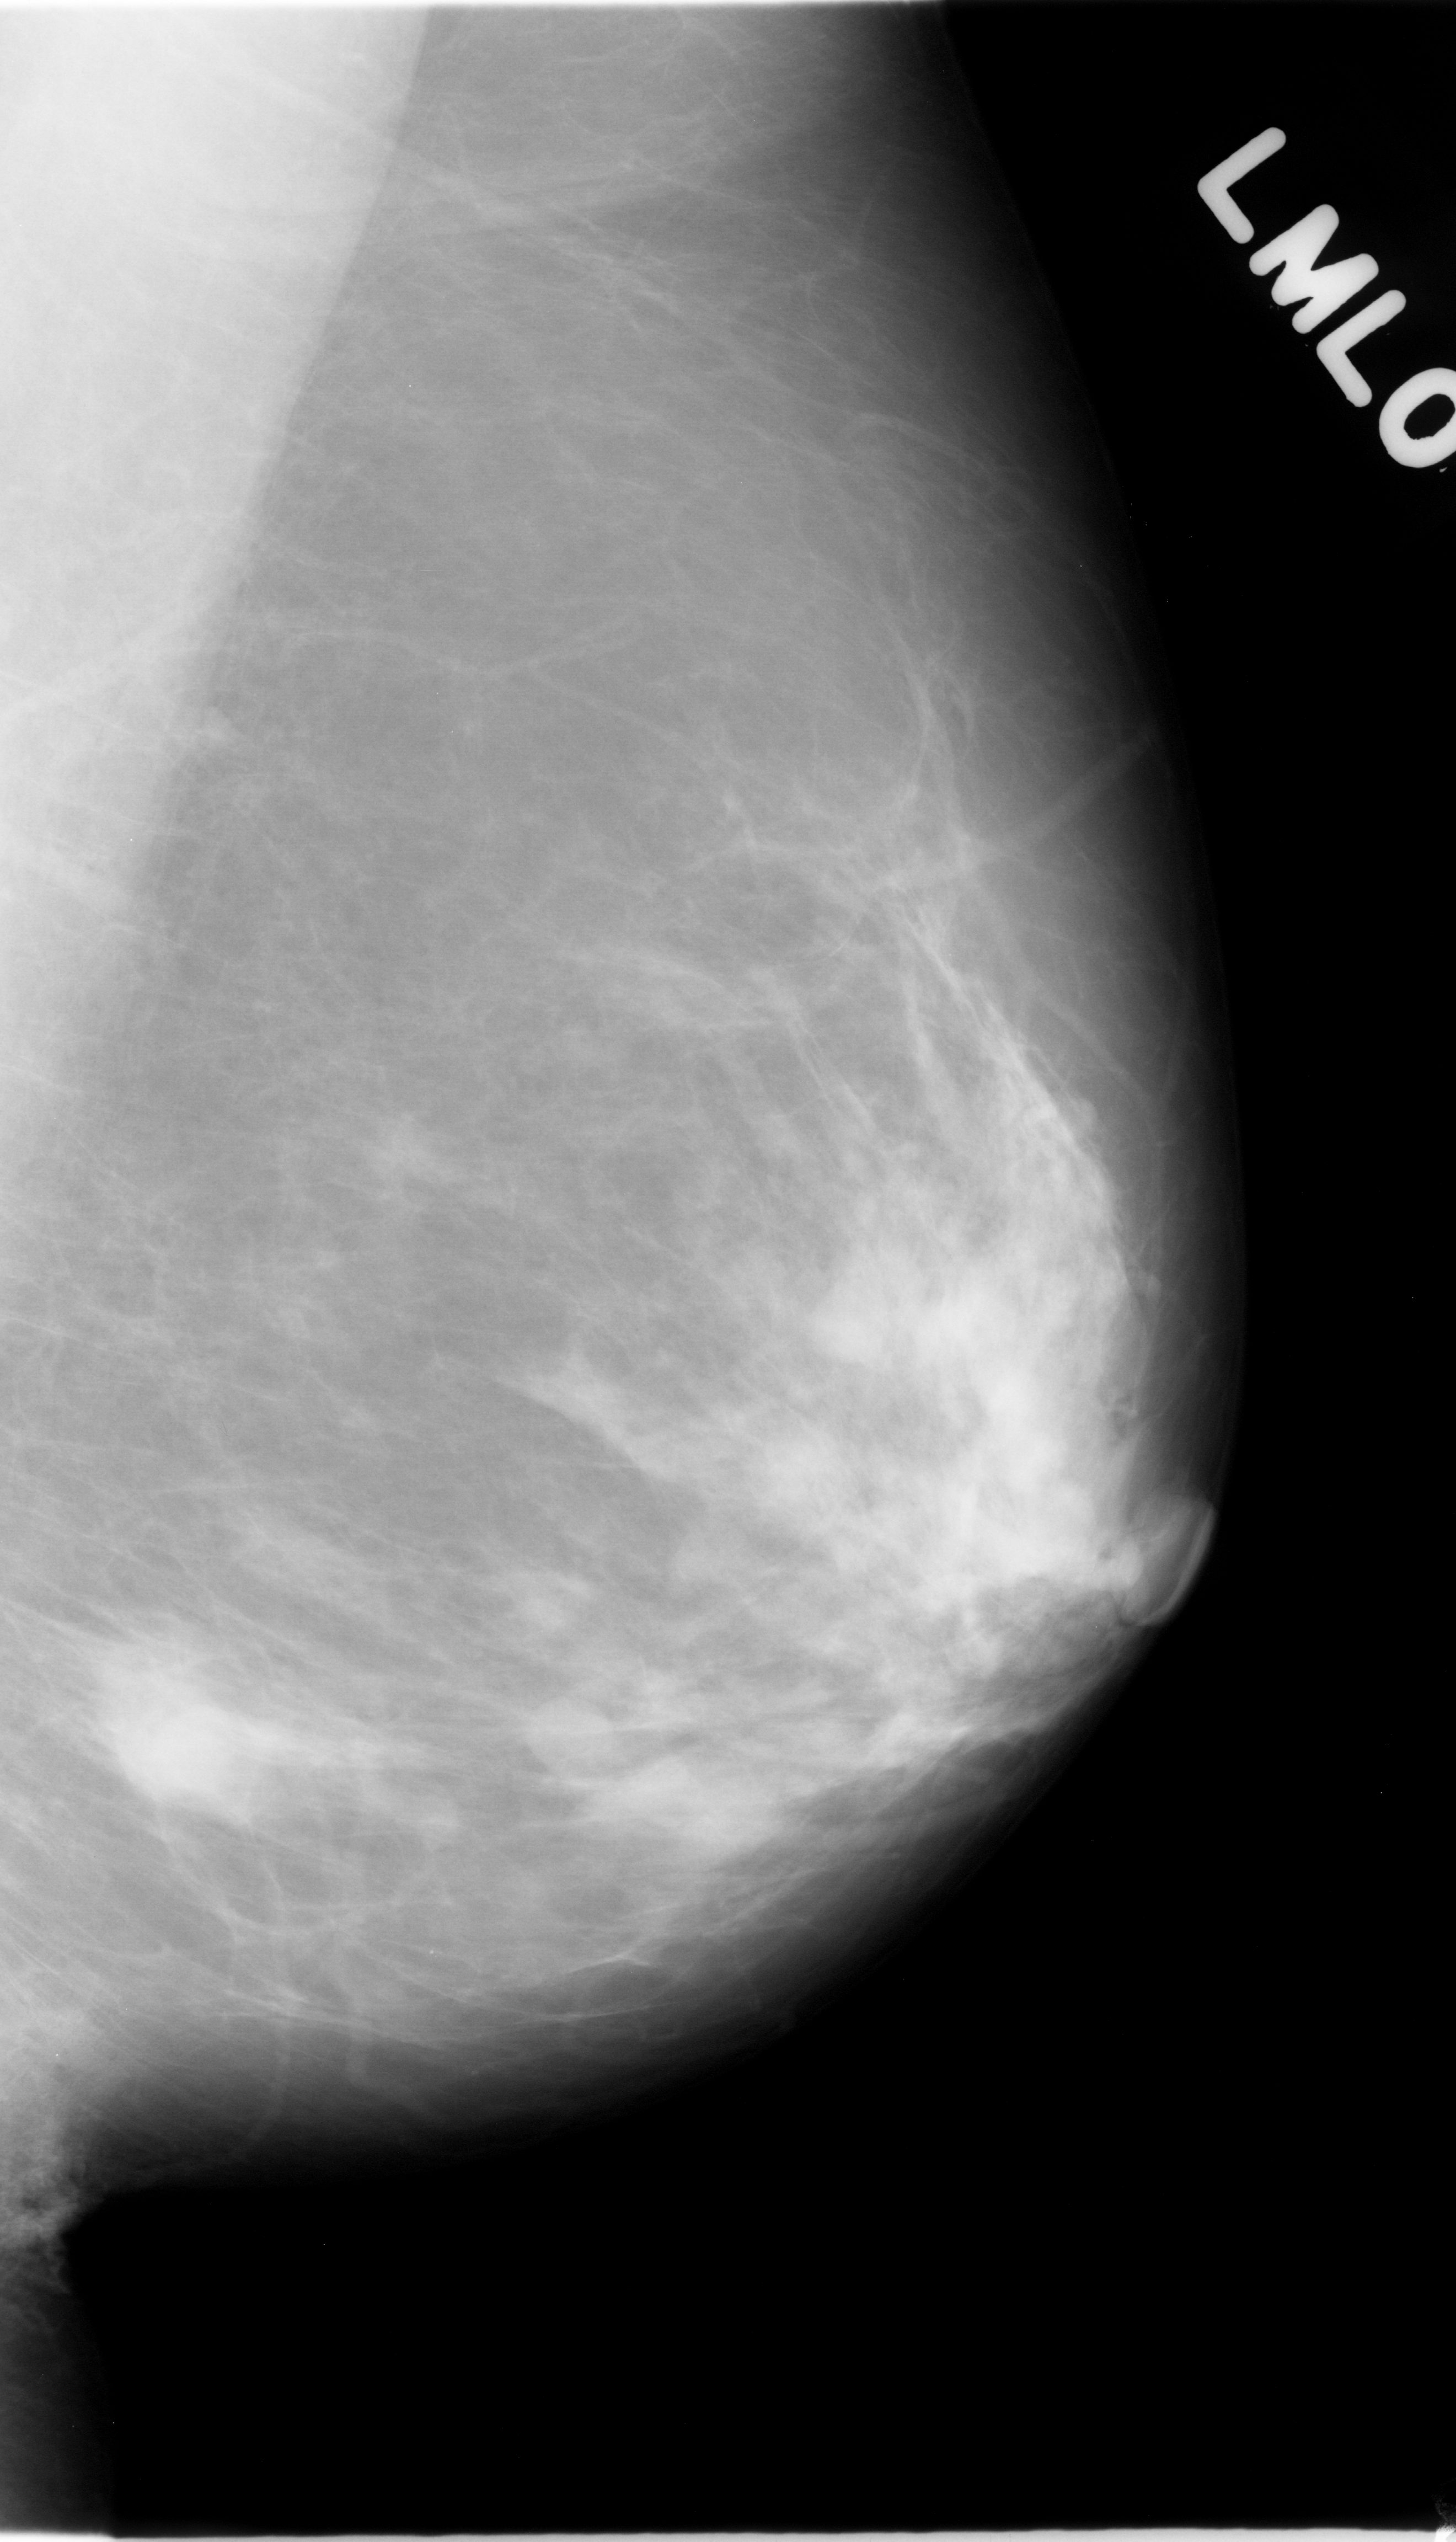
Digitized screen-film mammogram; left breast; mediolateral oblique (MLO) view; breast composition: scattered fibroglandular densities (BI-RADS density category 2 of 4).
- Radiologist-marked abnormalities on this image: Finding 1 of 2: mass, margins ill defined; BI-RADS assessment category 5; pathology result (as recorded, not read from the image): malignant.
- Finding 2 of 2: mass, shape oval, margins circumscribed; BI-RADS assessment category 3; pathology result (as recorded, not read from the image): benign.